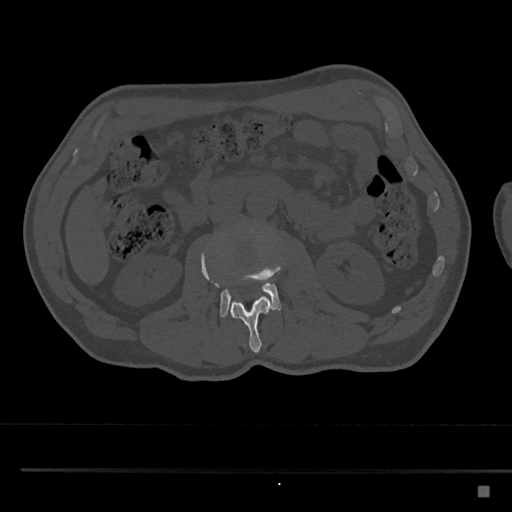
CT including the spine, one axial slice; position 733 of 797 along the scan axis; 120 kVp; bone window (W 1800 / L 400 HU); 0.5 mm slice thickness; 512 × 512 image matrix, field of view 391 × 391 mm. Patient: male, 59 years. Case-level facts recorded for this patient, not image findings: primary cancer: prostate.
Outlined on this slice (semi-automatically segmented with operator editing):
- L2 vertebra: bounding box (x1, y1, x2, y2) in pixels: (201, 237, 280, 353)
- L3 vertebra: (201, 228, 282, 318)